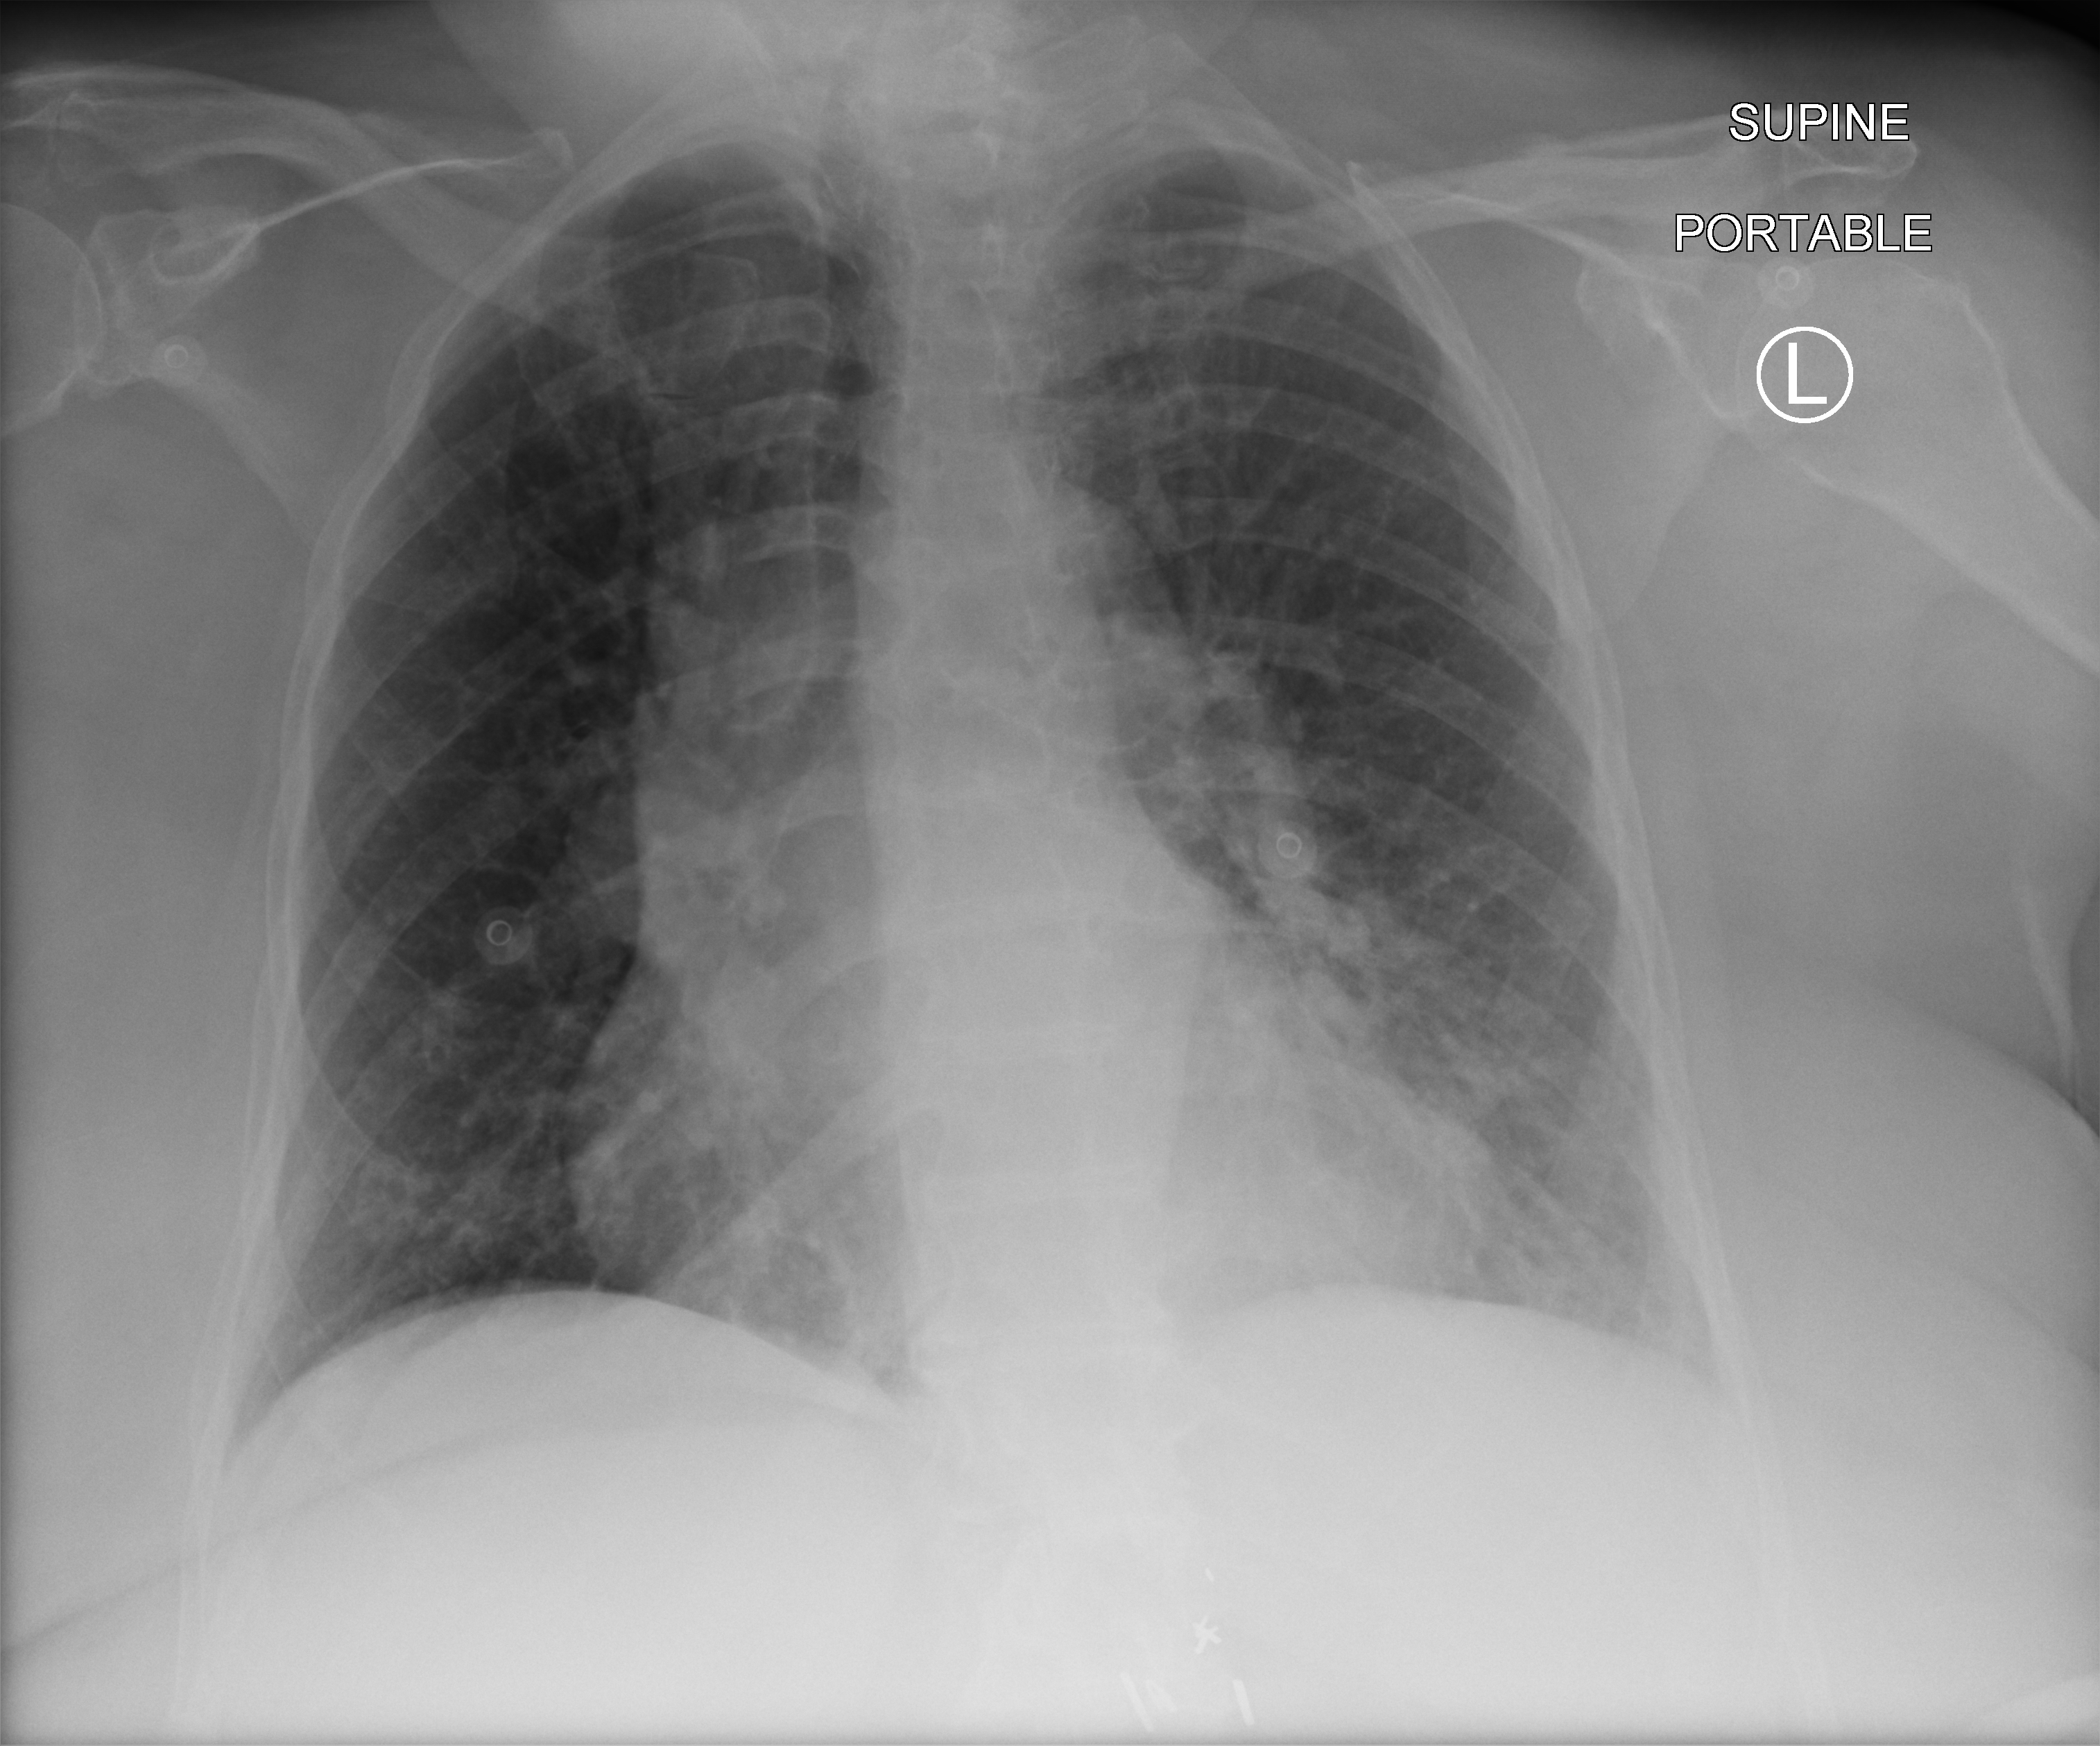
Bedside chest radiograph (computed radiography); anteroposterior (AP) projection. Female patient hospitalised with COVID-19, age 75–90 years.
From the hospital-stay record, not from the radiograph (when in the stay this image was taken is not recorded):
- COPD (admission record): no
- admitted to intensive care during this hospital stay: no